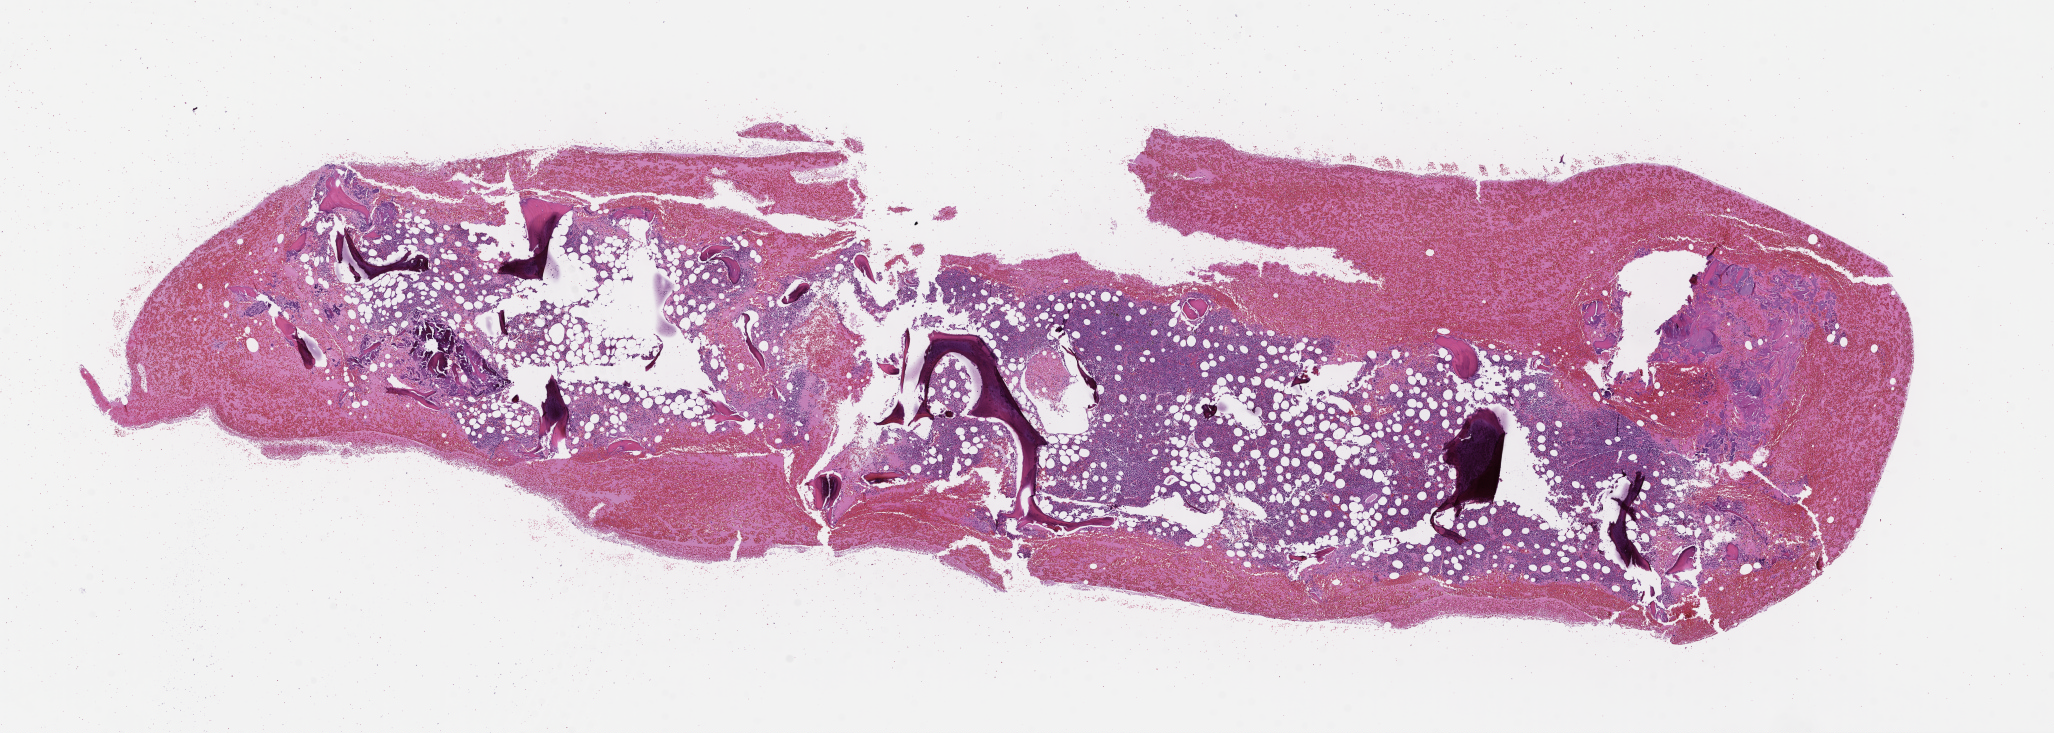
Whole-slide image, haematoxylin and eosin stain — shown as a low-resolution overview of the whole scanned area (about 16.6 x 5.9 mm). FFPE section. Site: bone marrow. Archival tissue. Patient sex: male.
This section: primary tumor. Diagnosis: Plasma Cell Myeloma.